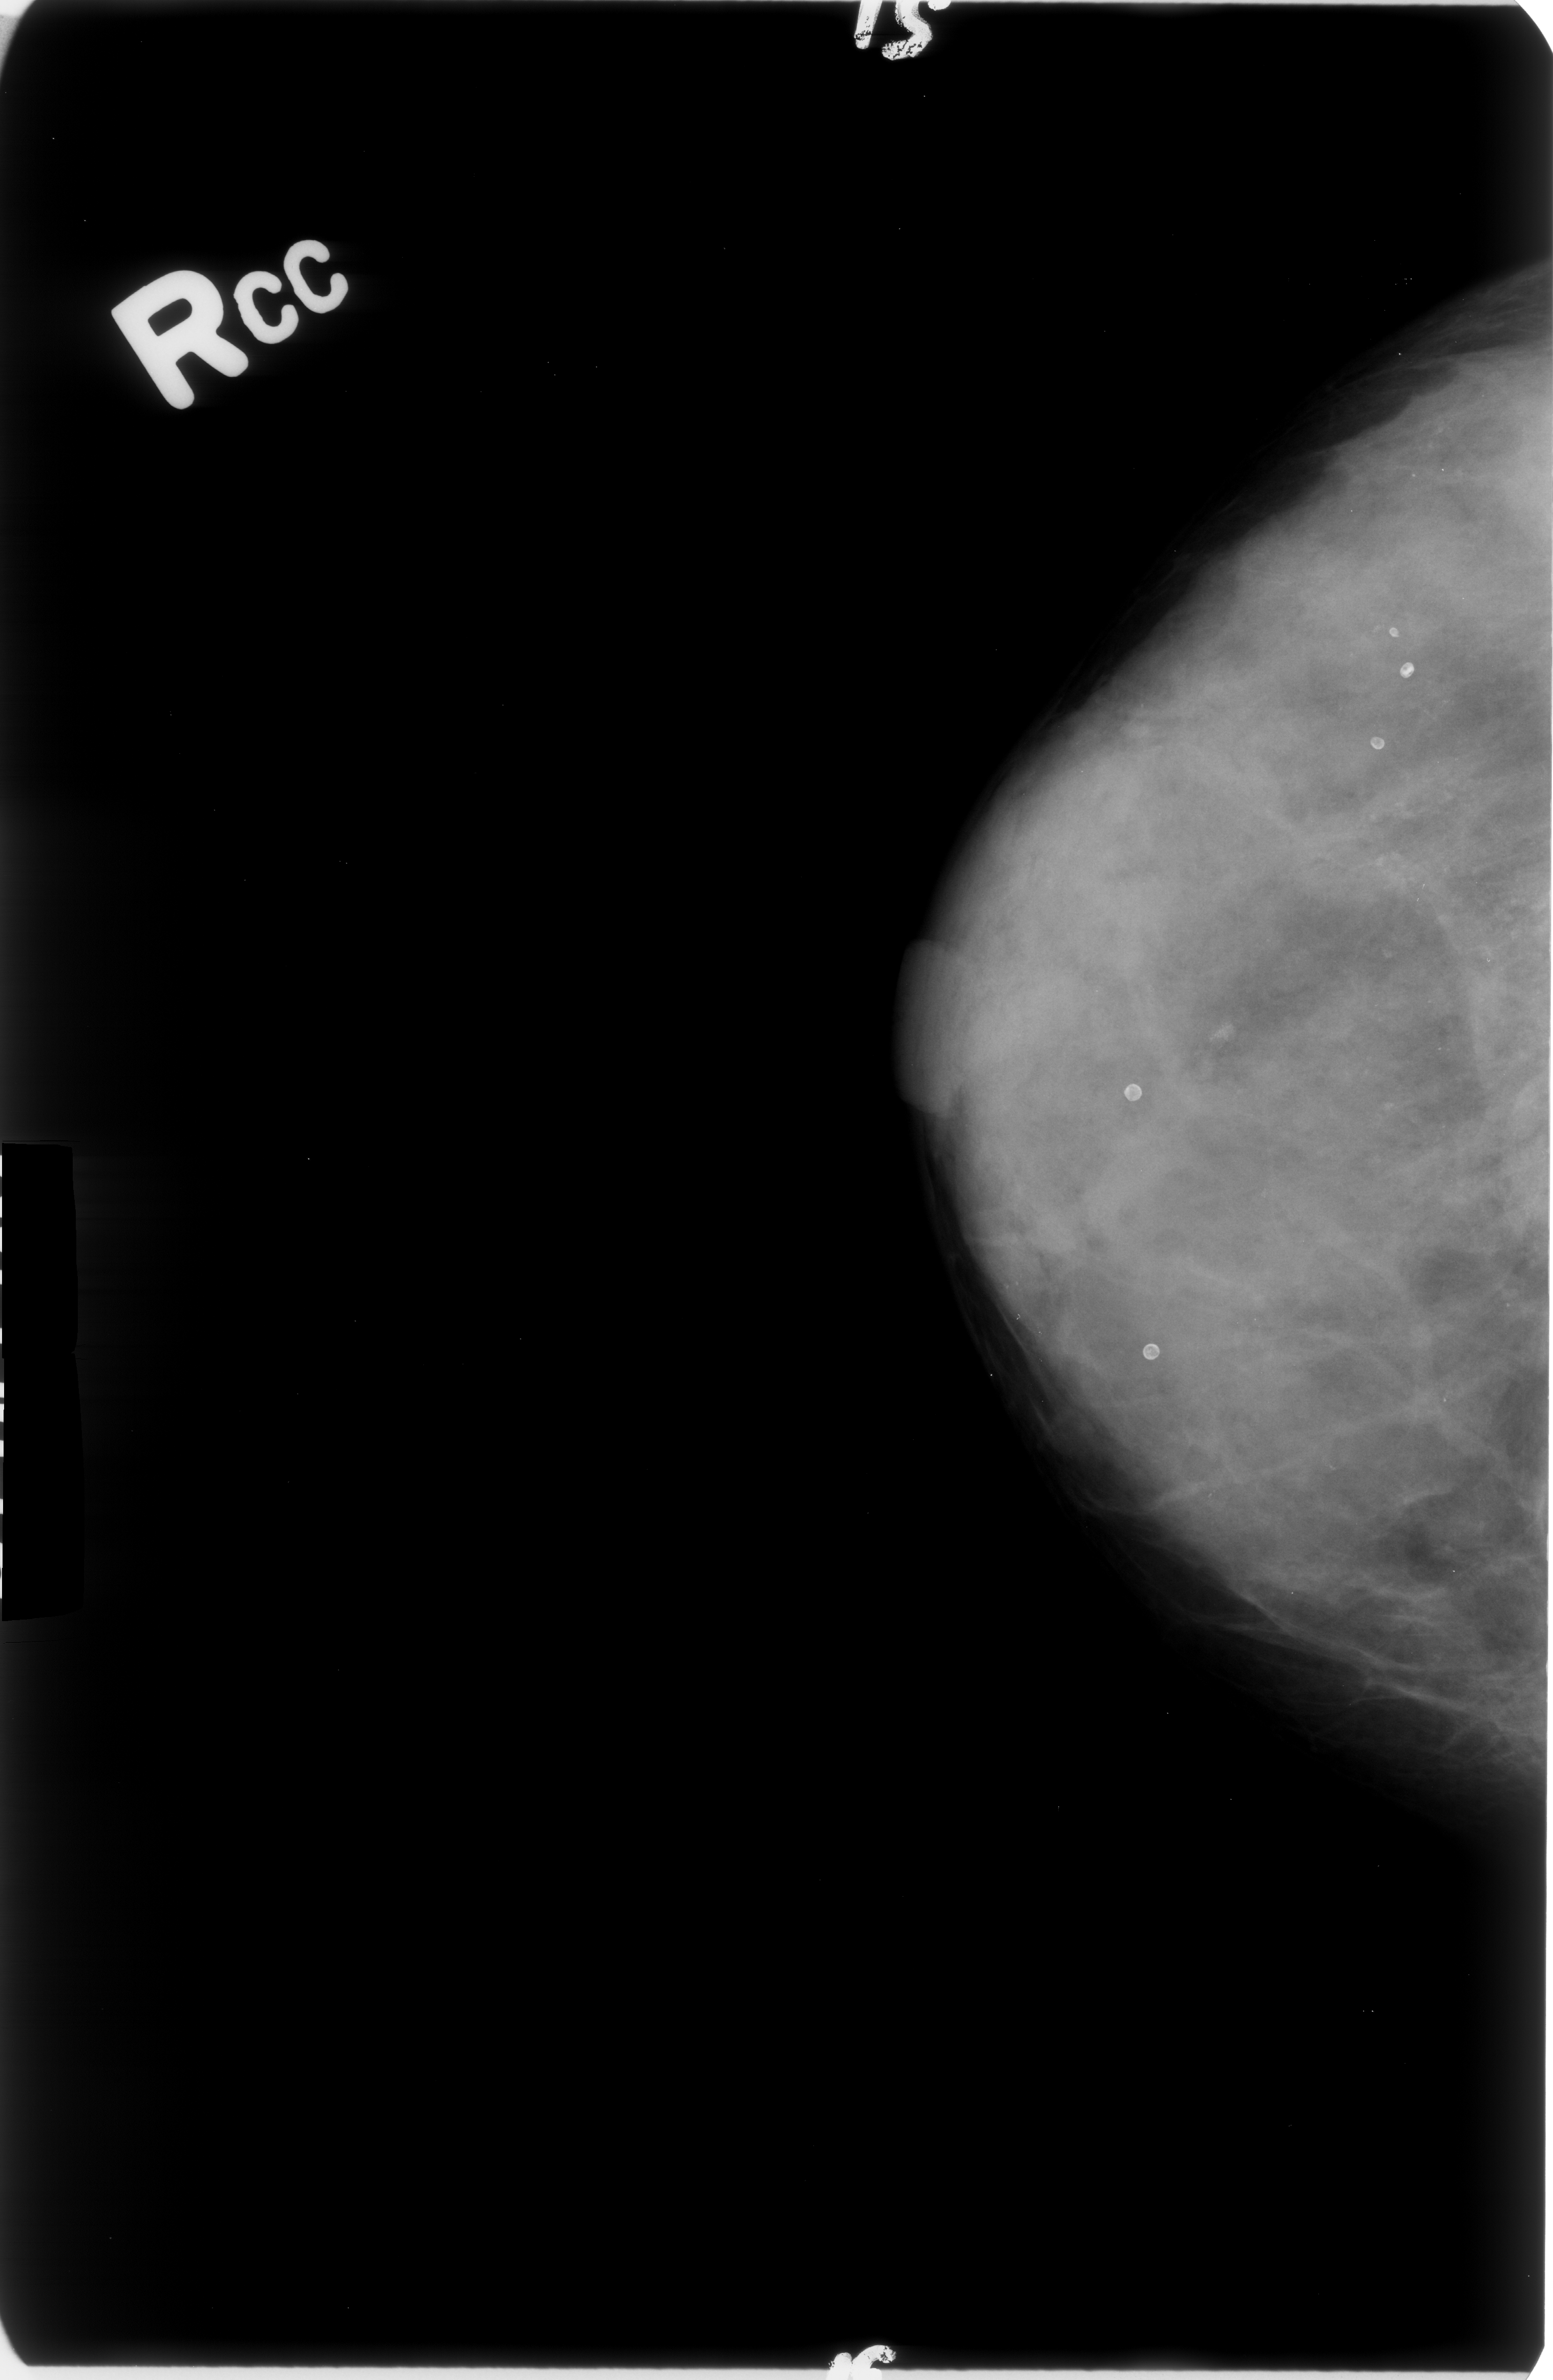
Digitized screen-film mammogram, right breast, craniocaudal (CC) view, BI-RADS breast density category 4 (scale 1–4).
Radiologist-marked abnormalities on this image: Finding 1 of 2: calcifications, morphology punctate / amorphous, distribution regional; BI-RADS assessment category 4; pathology (as recorded): benign. Finding 2 of 2: calcifications, morphology punctate / amorphous, distribution clustered; BI-RADS assessment category 4; subtlety rating 4 on a 1 (subtle) to 5 (obvious) scale; pathology result (as recorded, not read from the image): benign.